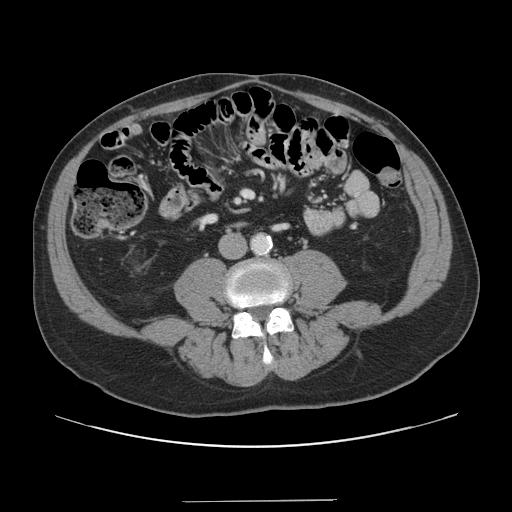
Contrast-enhanced abdominal CT, one axial slice; slice 14 of 151 in the series (ordered by position); 120 kVp; soft-tissue window (W 400 / L 40 HU); 512 × 512 image matrix. Male patient, age 63 years. From the clinical record (not read from this slice): diagnosis: colorectal cancer liver metastases, imaged before liver resection; multiple liver metastases: no; largest metastasis: 2.1 cm; disease in both lobes: no.
Annotated regions visible in this slice (manually delineated by an expert):
- portal vein (with intrahepatic branches): bounding box [x1, y1, x2, y2] px = [244, 193, 253, 197]